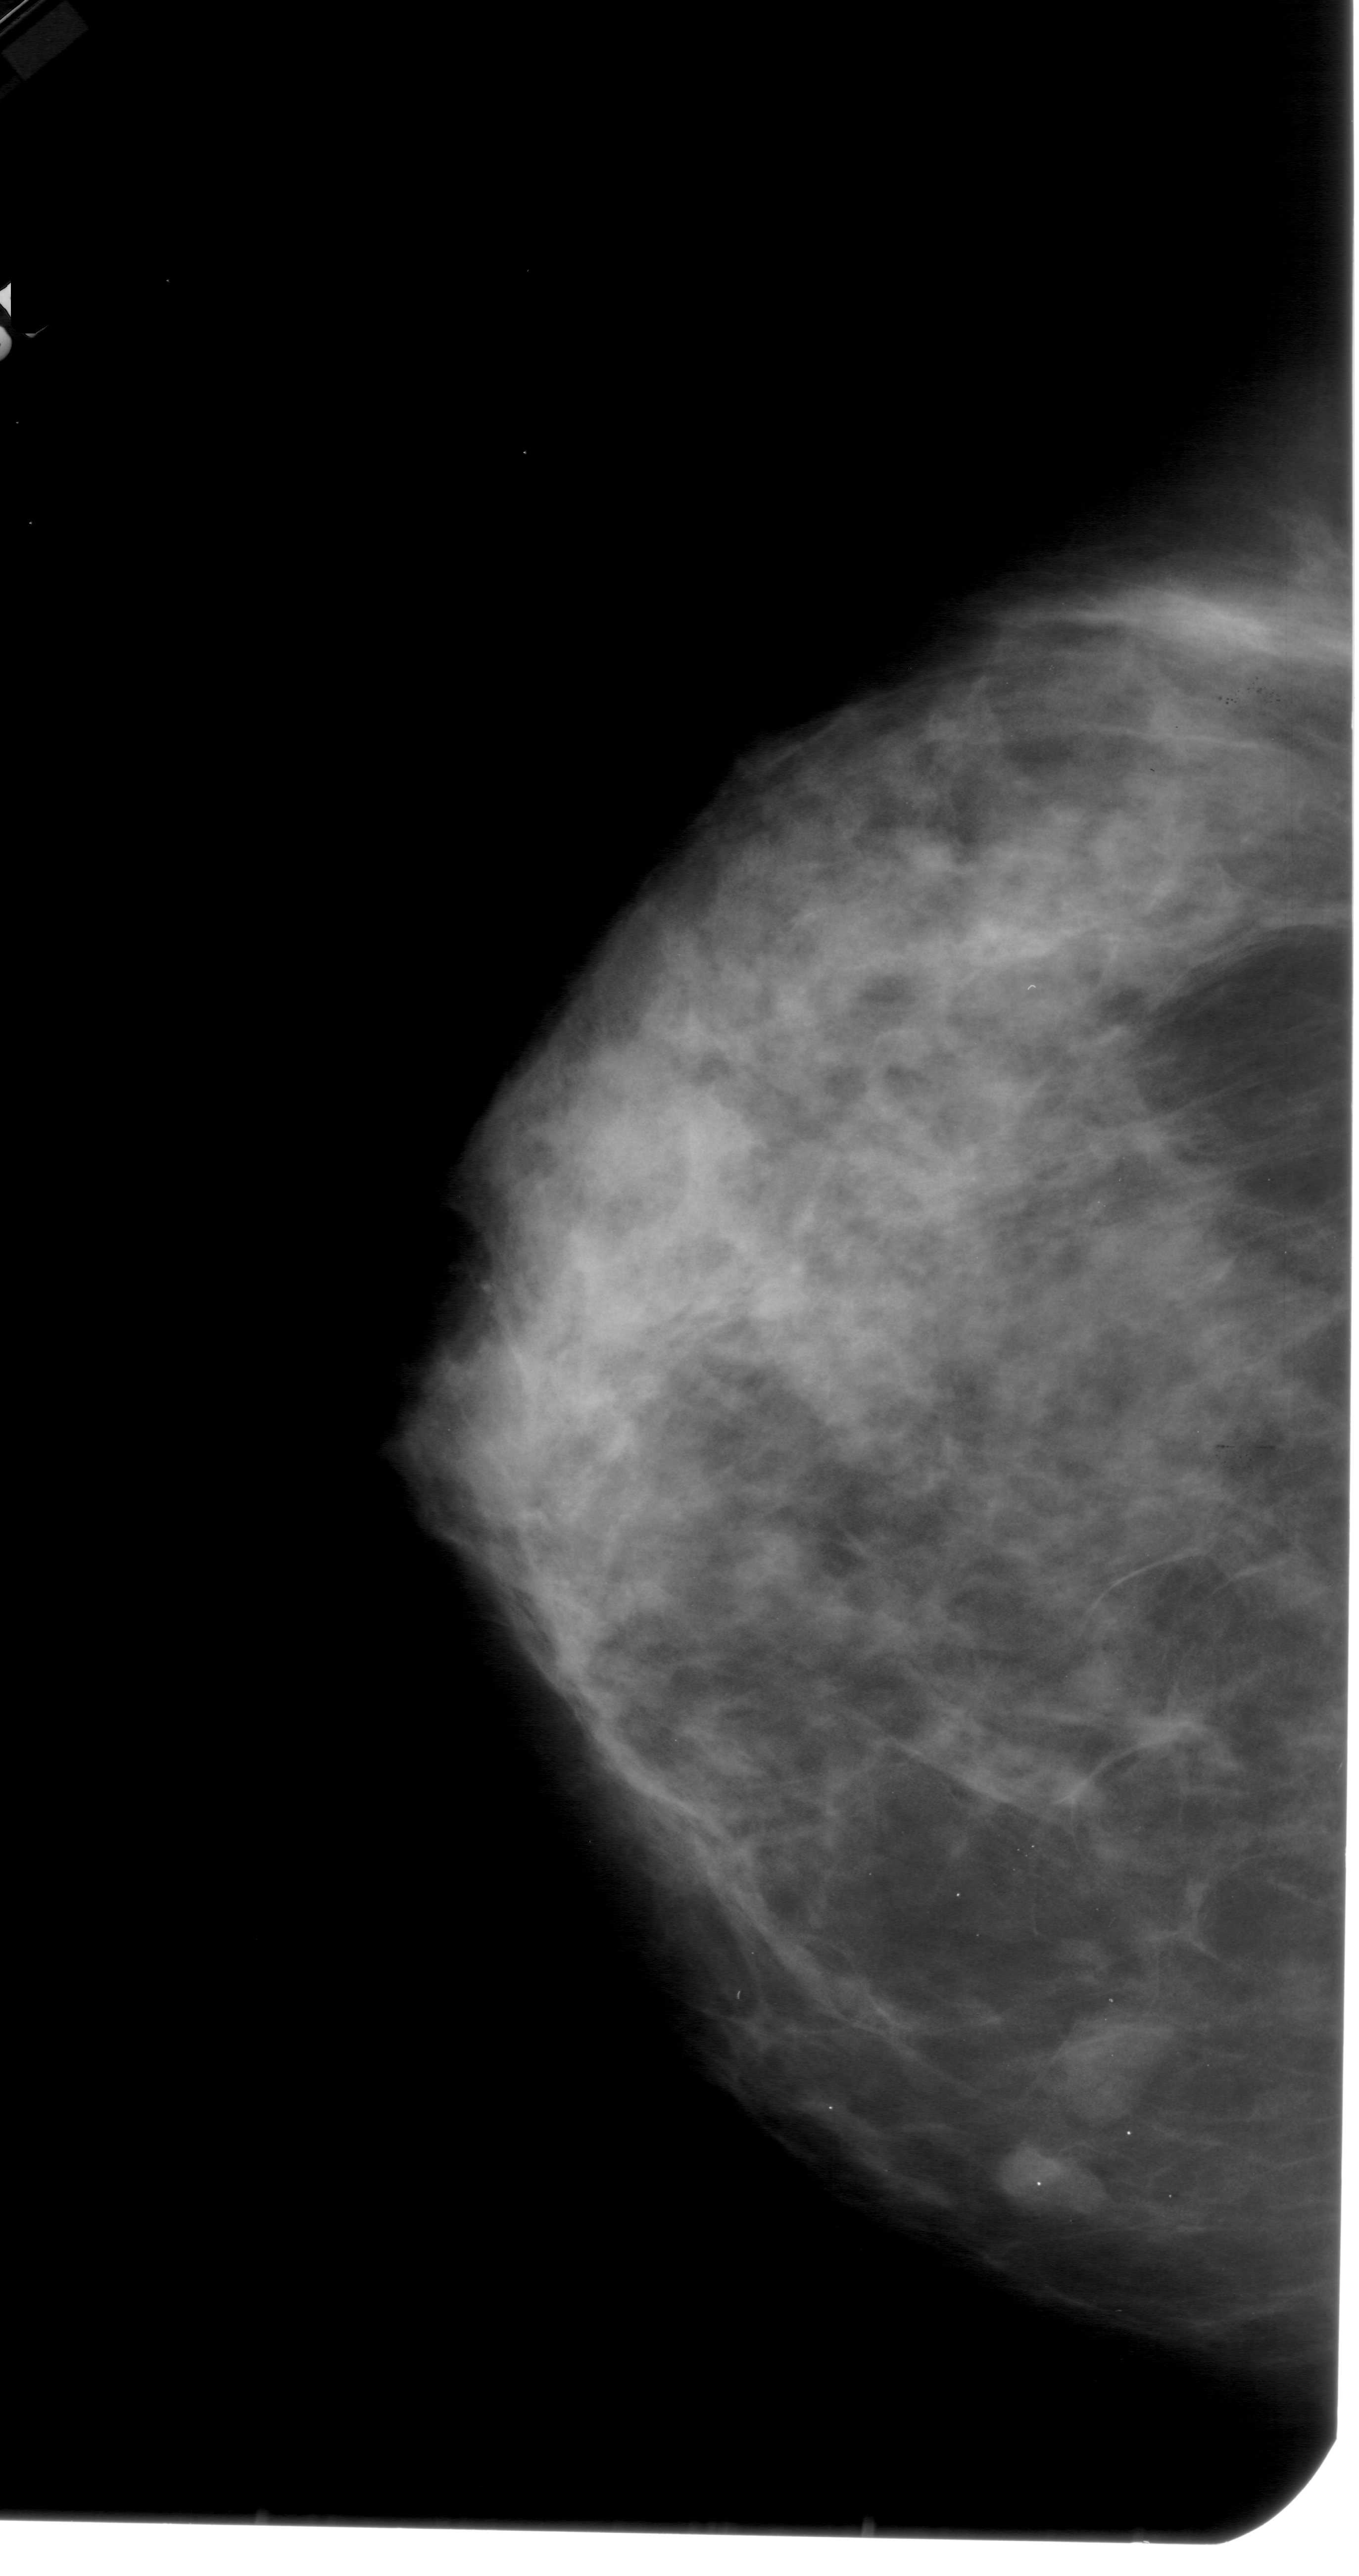
Digitized screen-film mammogram; left breast; CC view; BI-RADS breast density category 3 (scale 1–4).
Radiologist-marked abnormalities on this image: mass, shape lobulated, margins circumscribed; BI-RADS assessment category 4; subtlety rating 3 on a 1 (subtle) to 5 (obvious) scale; pathology result (as recorded, not read from the image): benign.